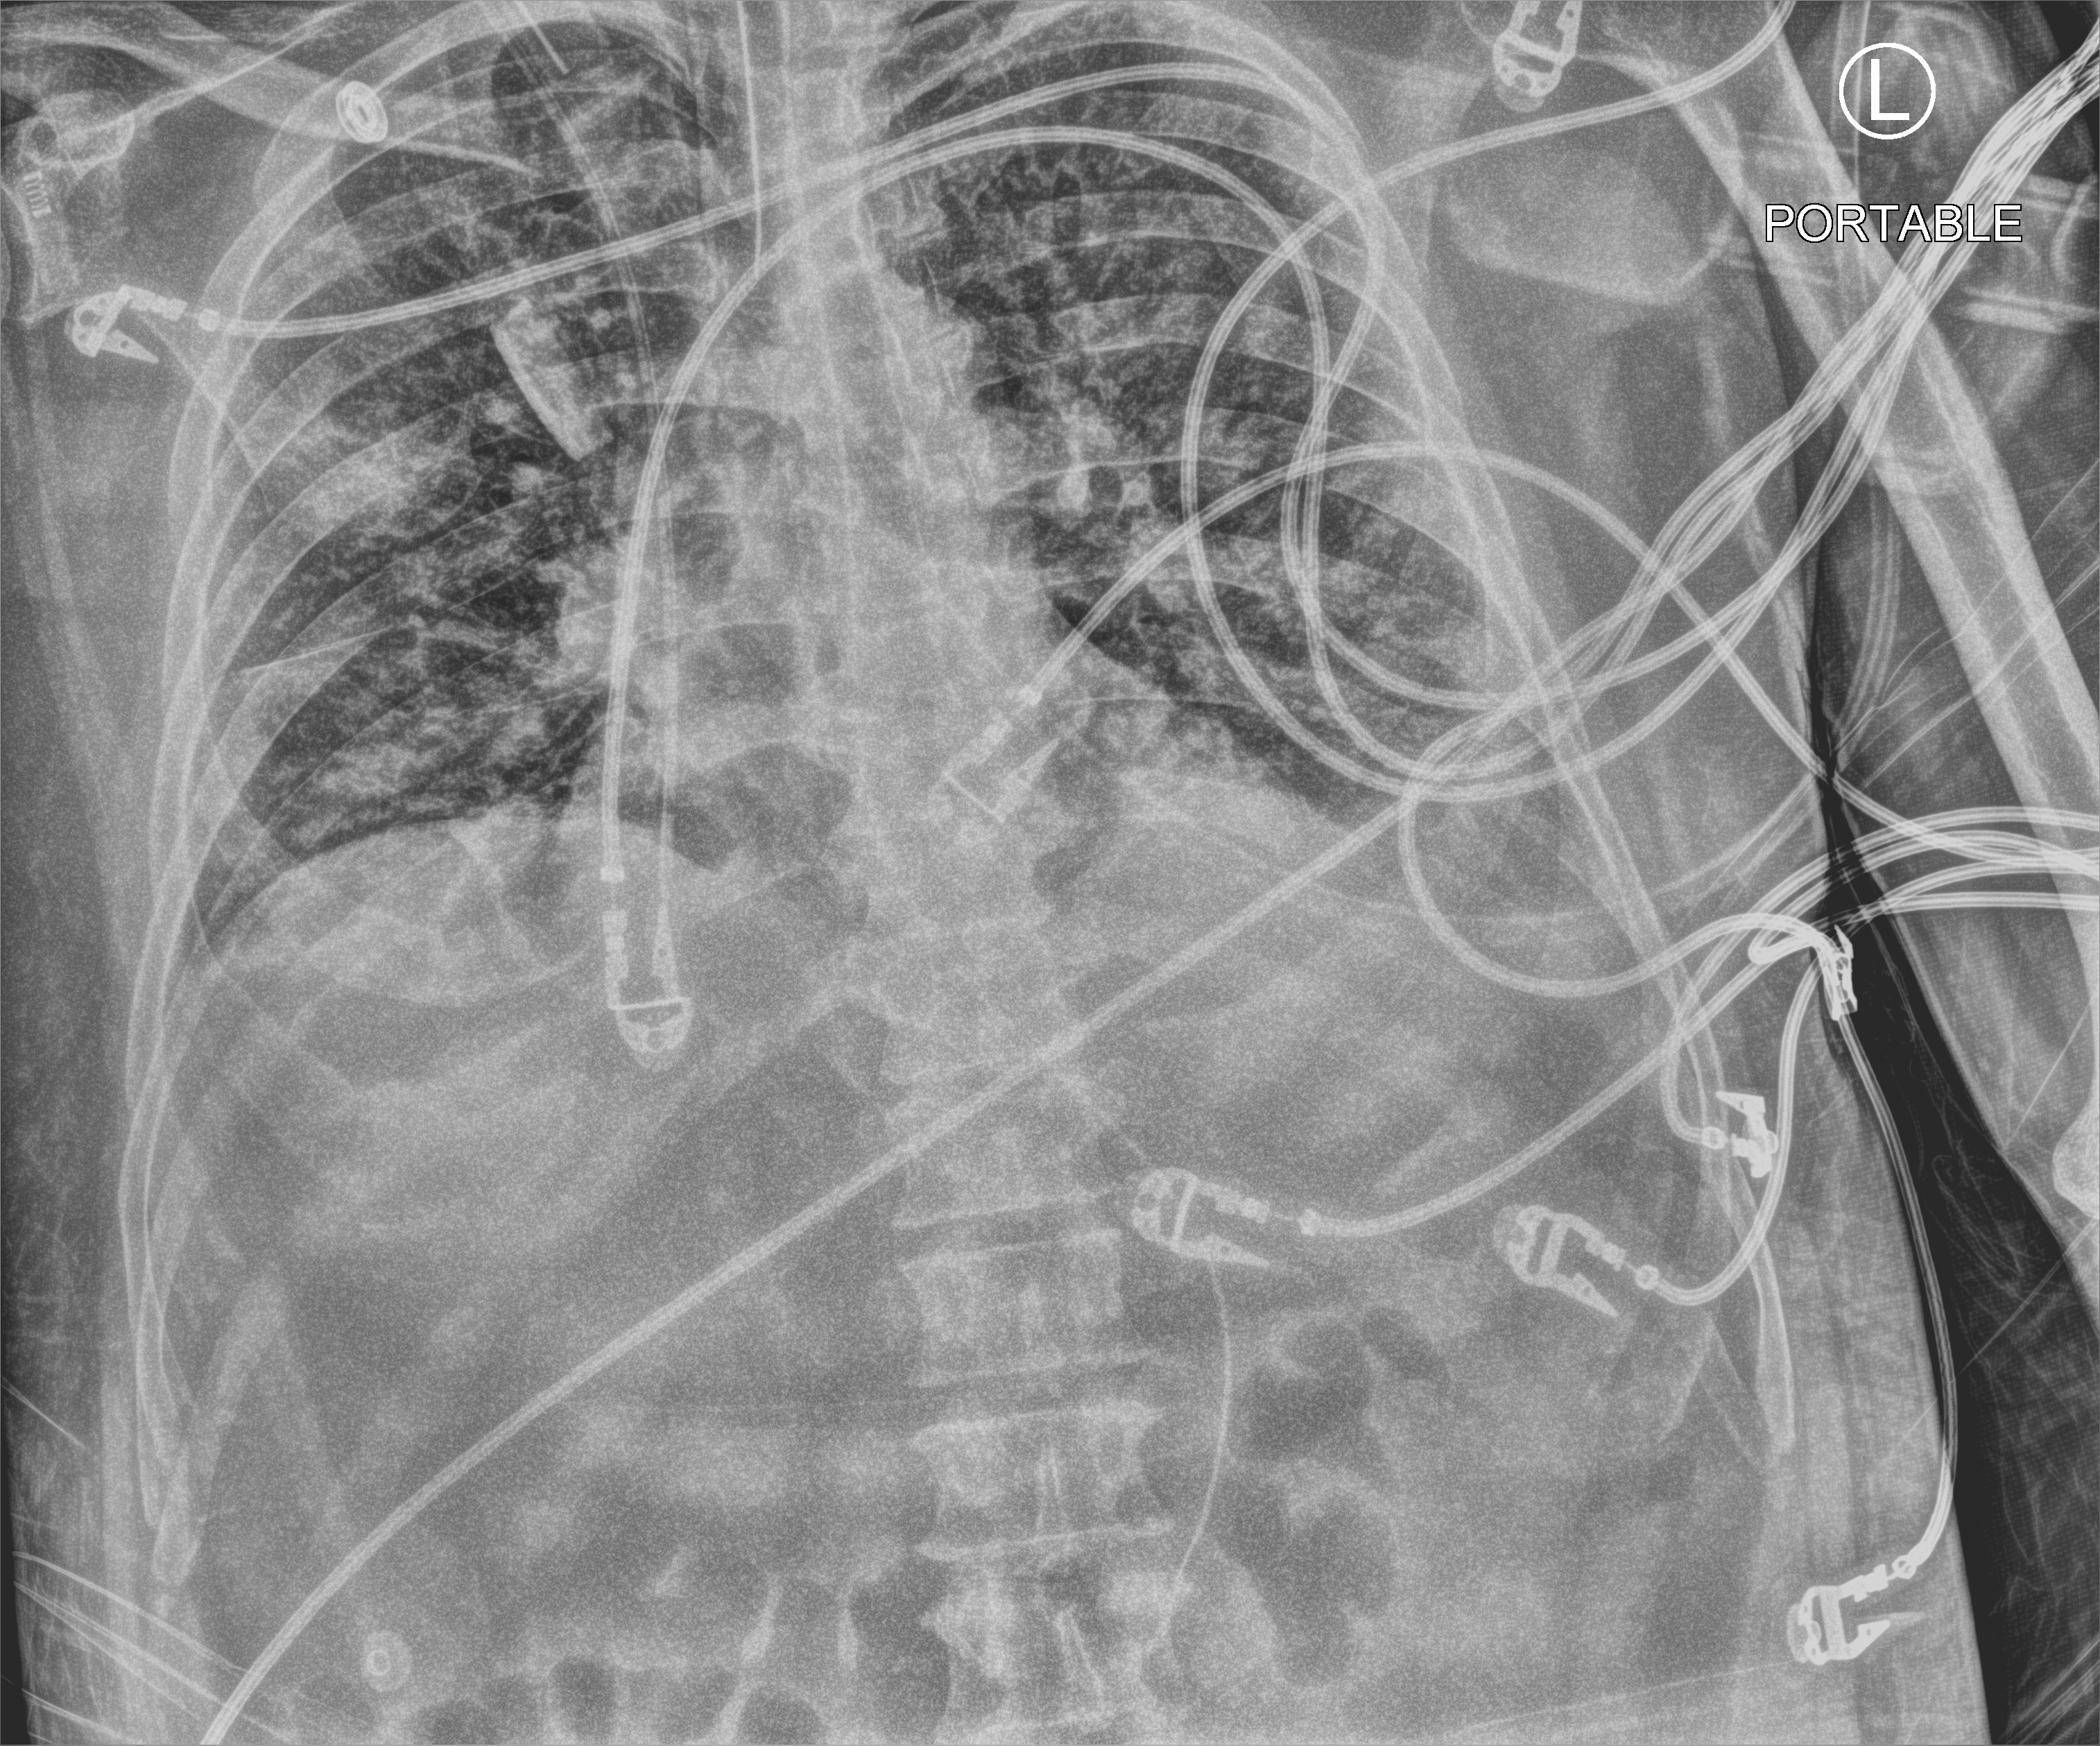
Chest X-ray (portable), anteroposterior (AP) projection. Male patient hospitalised with COVID-19, age 18–59 years.
From the hospital-stay record, not from the radiograph (when in the stay this image was taken is not recorded): smoking status (admission record): former.